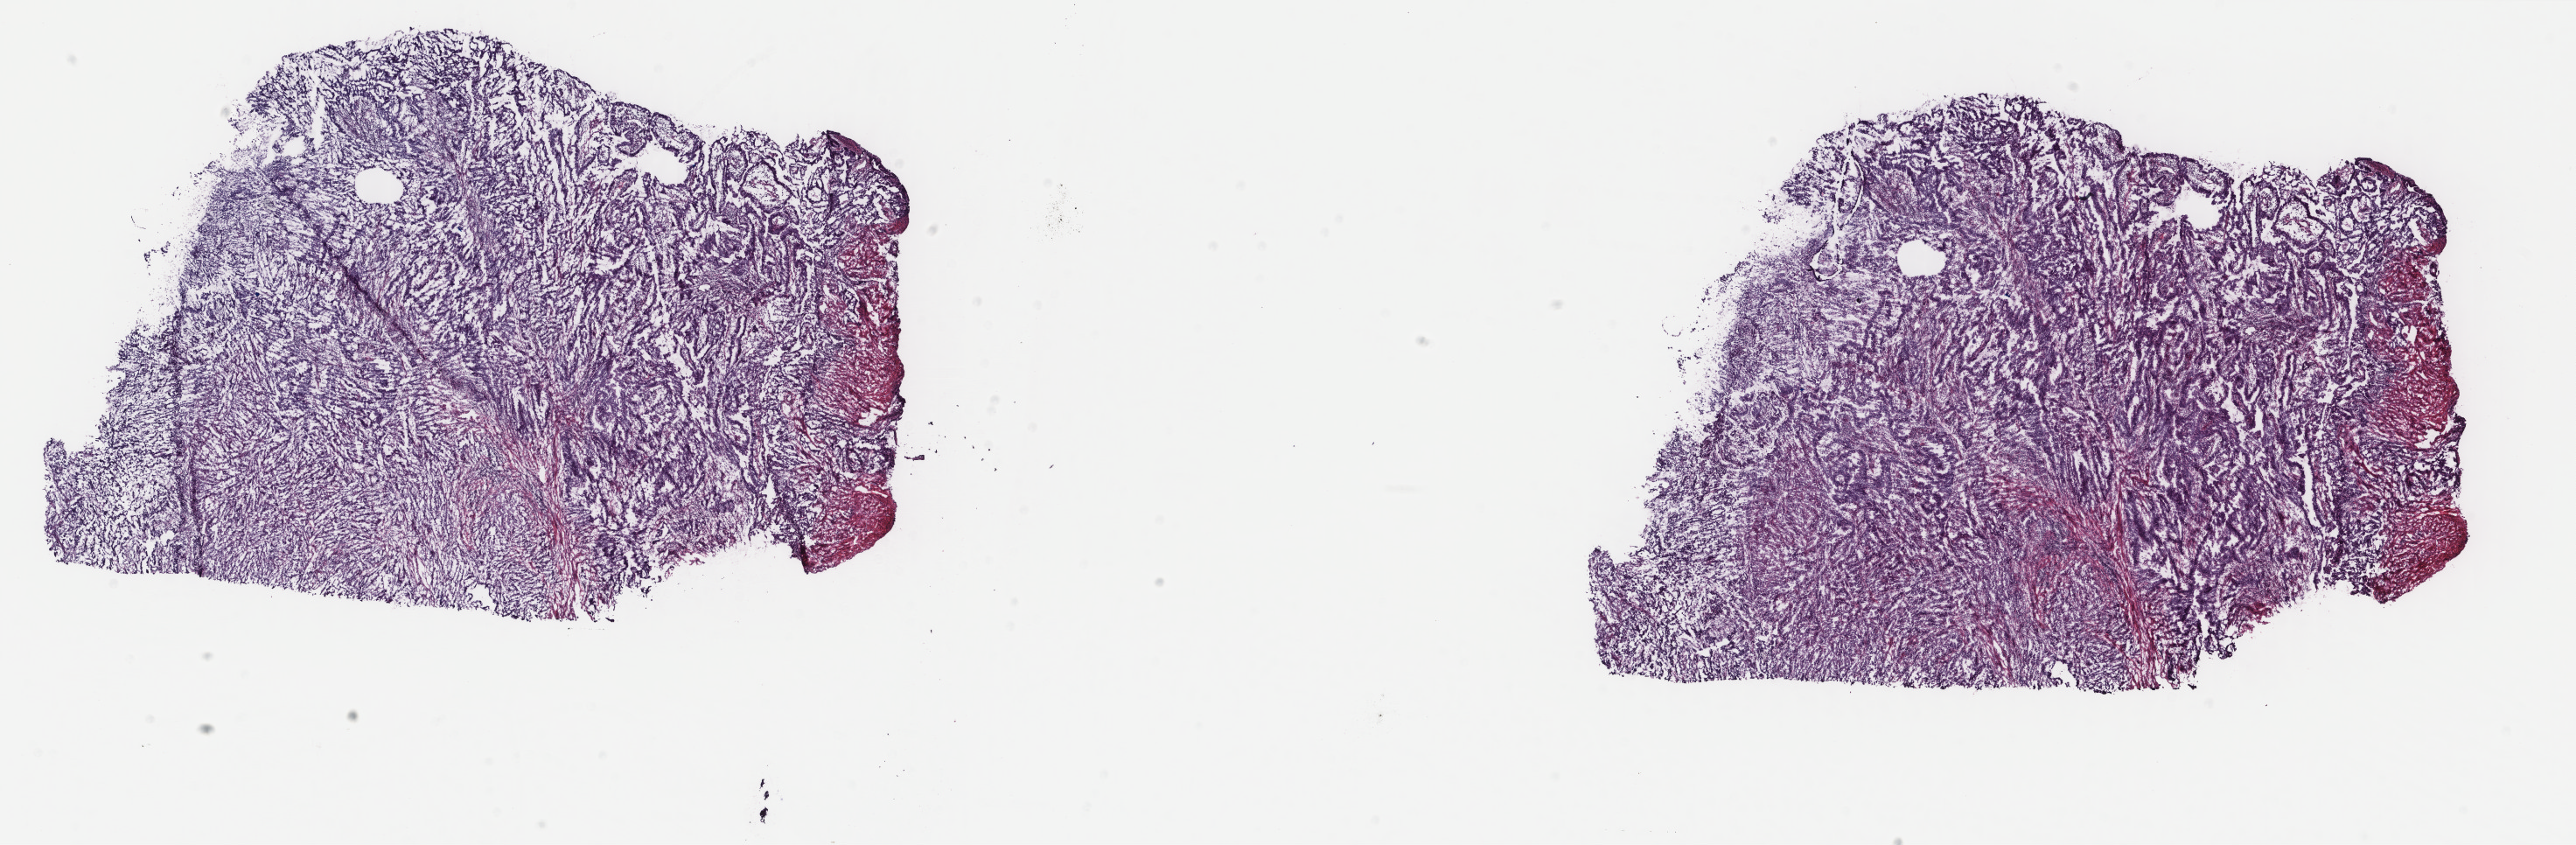
H&E-stained whole-slide image, shown as a low-resolution overview of the whole scanned area (about 23.4 x 7.7 mm); frozen section from the top of the tissue portion; sample: primary tumour, uterus. Female patient; age at initial diagnosis 65 years. Histologic grade: G3 (poorly differentiated). Pathologist review of this section (percent, as recorded): tumour cells 68%, tumour nuclei 65%, normal cells 10%, stromal cells 20%, necrosis 2%. Infiltration values recorded for this section: lymphocyte infiltration 20%, monocyte infiltration 1%, neutrophil infiltration 1%.
* lymph nodes positive (case pathology): 0 of 11 examined
* FIGO stage: IC
* histologic diagnosis: Serous cystadenocarcinoma, NOS (endometrium)